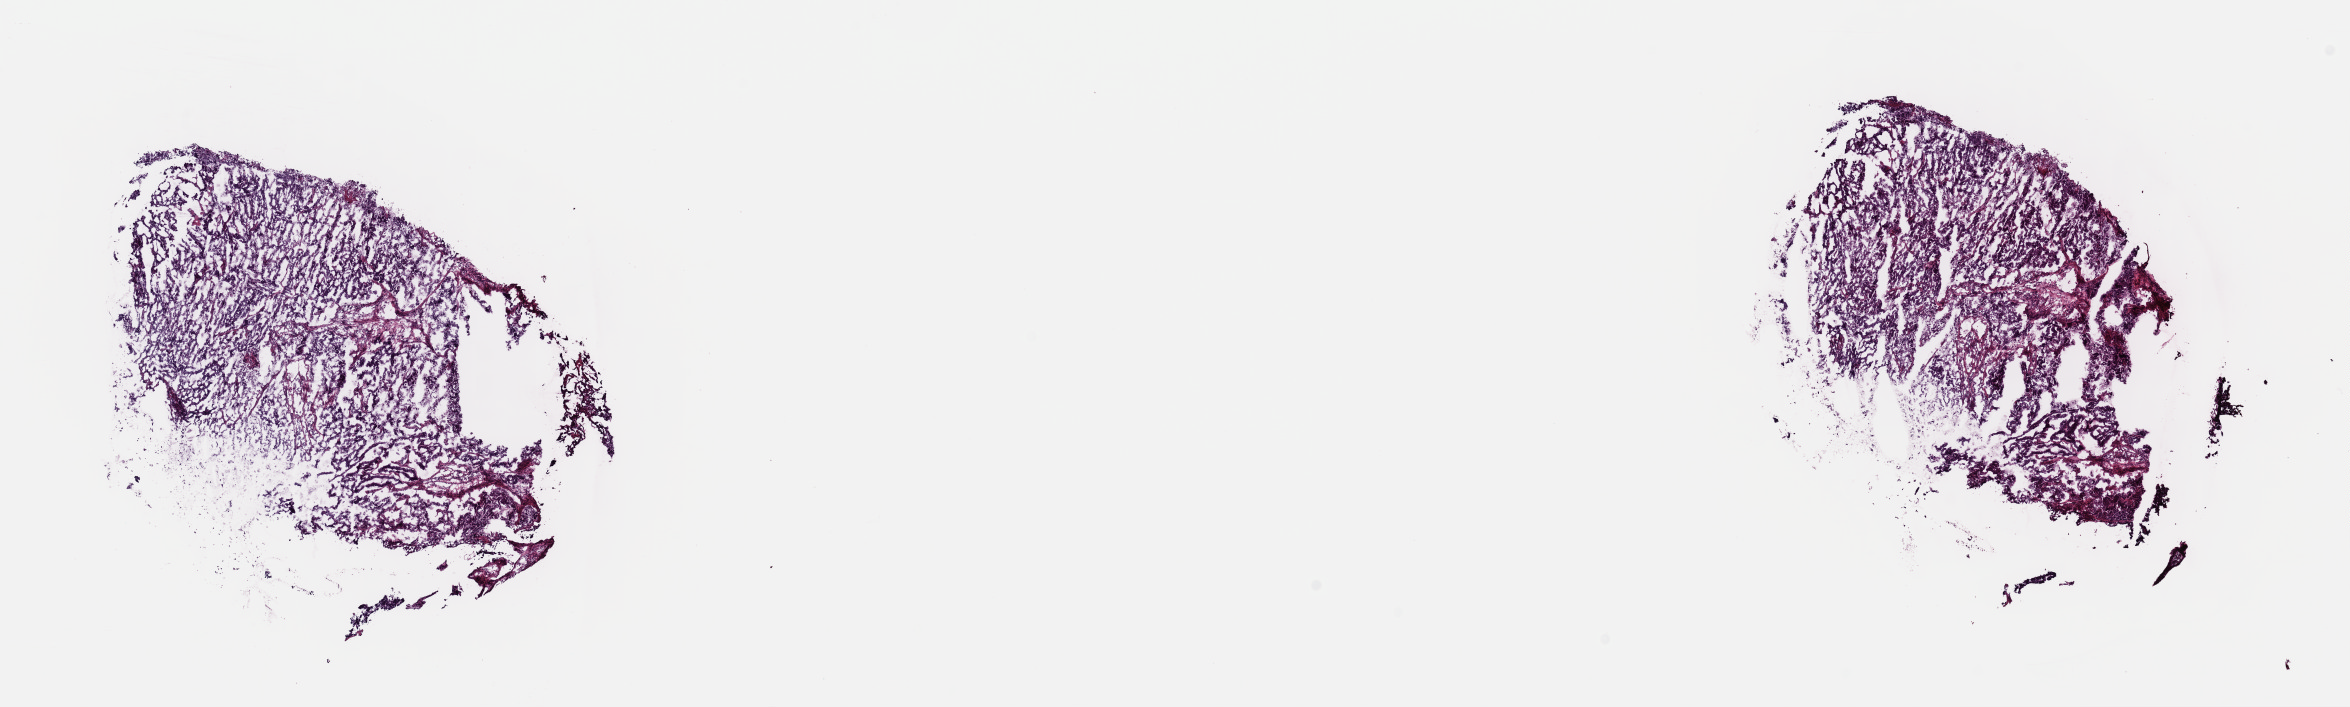
H&E-stained whole-slide image — a low-resolution overview of the entire scanned area, about 18.6 x 5.6 mm (slide scanned at 40x). Frozen section. Sample: primary tumour, uterus. Patient: female, age at initial diagnosis 35 years. Histologic grade: G3 (poorly differentiated). Slide review estimates, as recorded: tumour cells 80%, tumour nuclei 85%, normal cells 10%, stromal cells 7%, necrosis 3%. Inflammatory infiltration, as recorded: lymphocyte infiltration 6%, monocyte infiltration 0%, neutrophil infiltration 0%.
FIGO stage: IB. Histologic diagnosis: Endometrioid adenocarcinoma, NOS (endometrium).